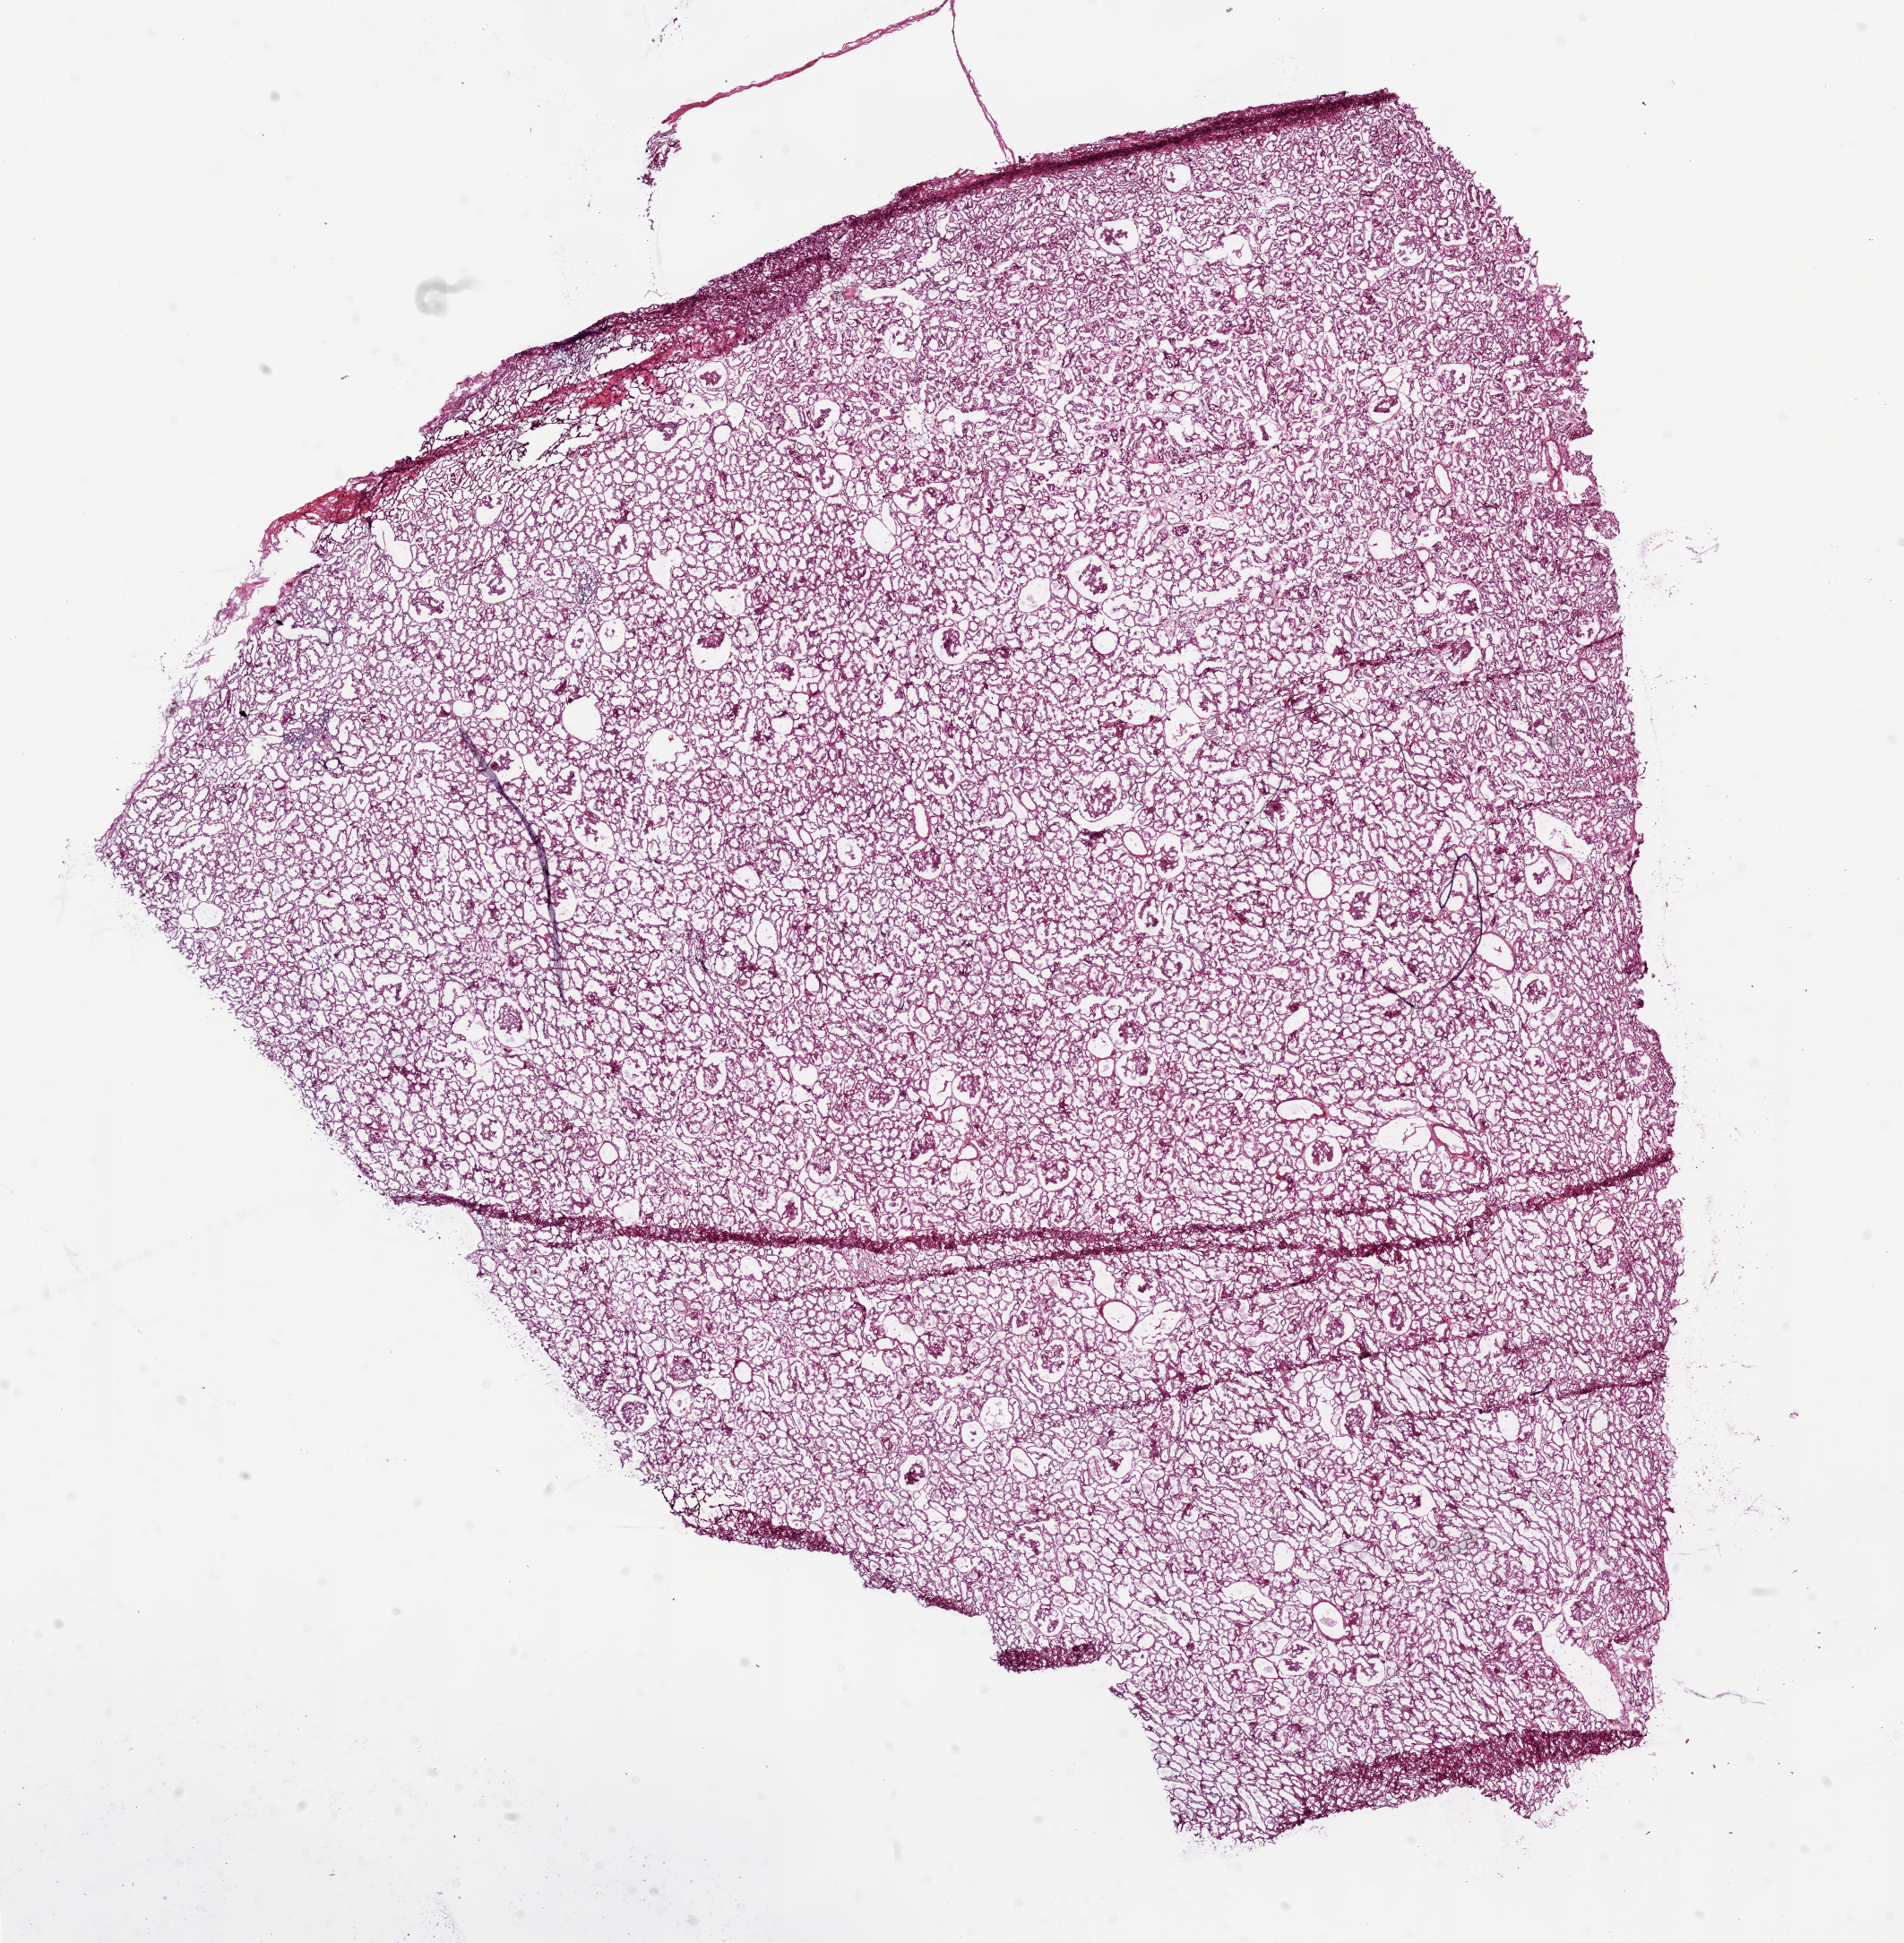
H&E whole-slide image — a low-resolution overview of the entire scanned area, about 17.1 x 17.4 mm. Frozen section. Sample: solid tissue normal (non-tumour tissue), kidney. Male, age 47 years at initial diagnosis.
This section: solid tissue normal (non-tumour) sample from the same patient. Patient diagnosis: Clear cell adenocarcinoma, NOS.